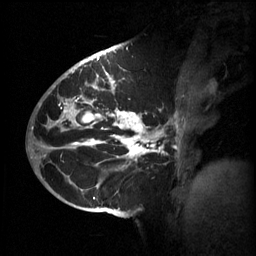
Breast MRI (dynamic contrast-enhanced), one sagittal slice; 3 images stored at this slice position (order not interpretable as contrast timing); 1.5 T; TE 4.2 ms, TR 11 ms; 256 × 256 image matrix, field of view 220 × 220 mm. Female patient, age 51 years.
Outlined on this slice (semi-automatically segmented with operator editing):
- analysis volume of interest (the breast-tissue region the enhancement analysis was run in; not a lesion): bounding box [x1, y1, x2, y2] px = [63, 80, 185, 201]
- tumour enhancement mask (voxels above the 70 % enhancement threshold inside the analysis volume of interest): [63, 80, 164, 199]